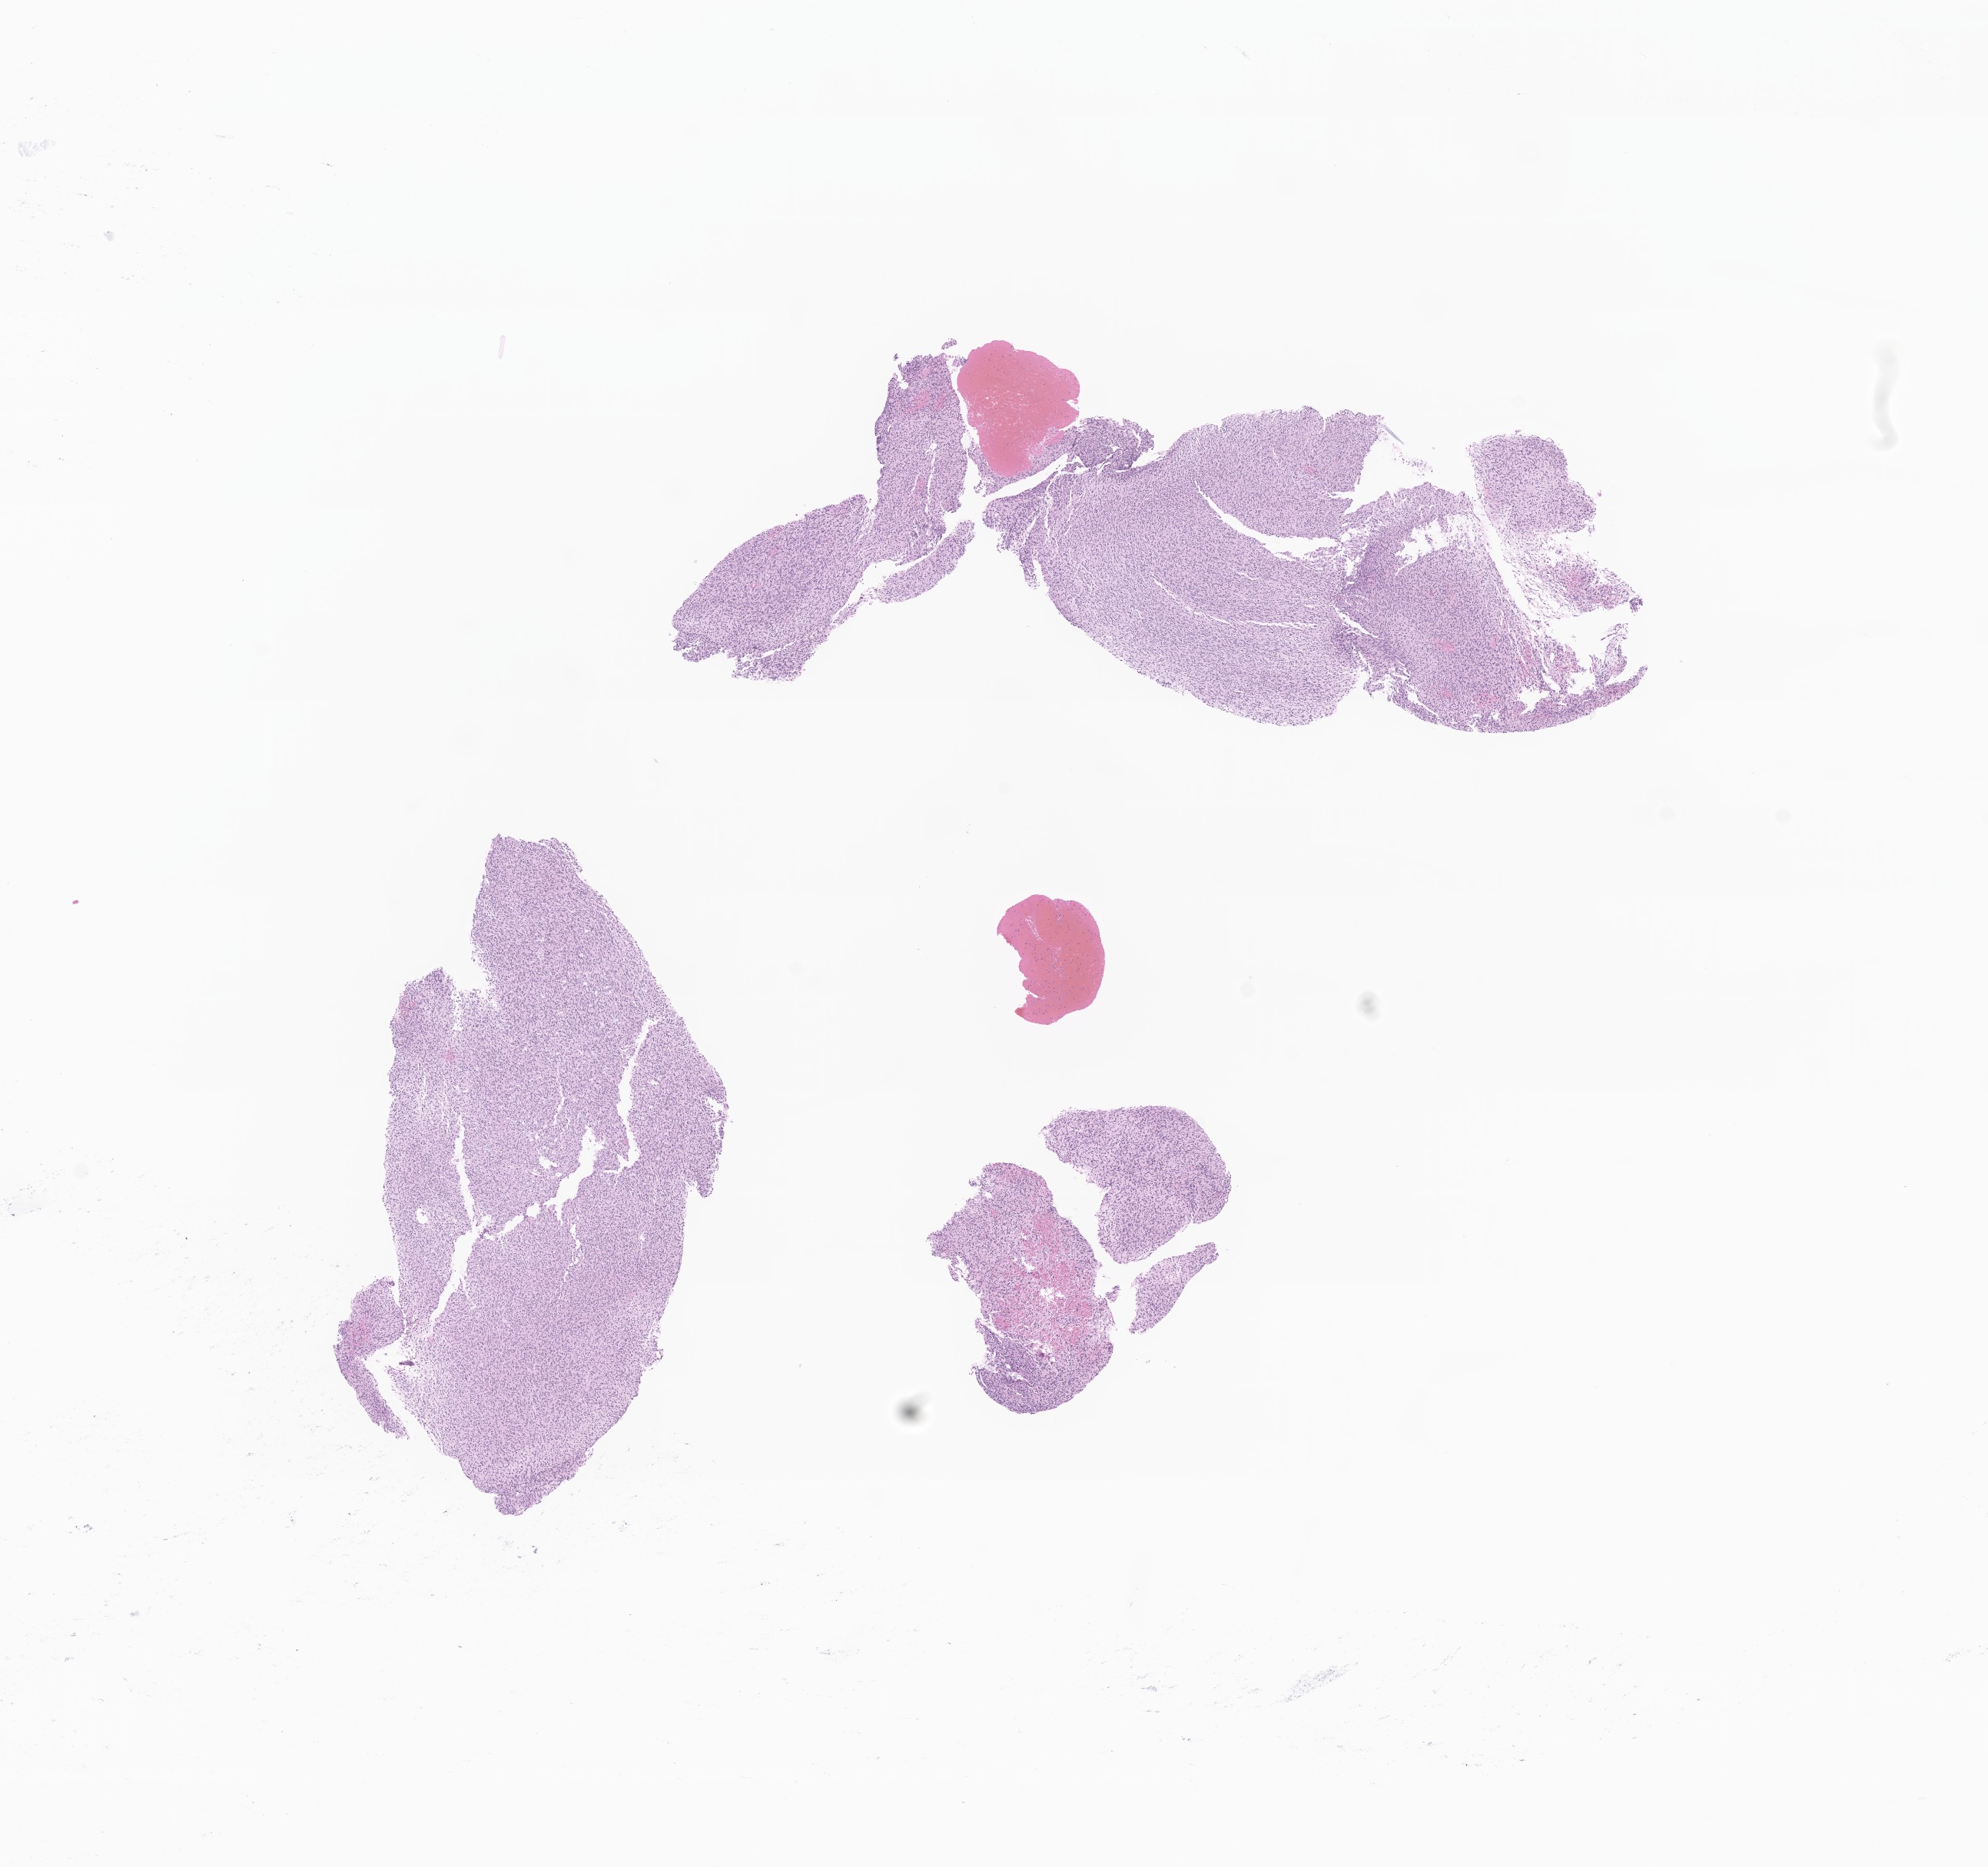
Whole-slide image, haematoxylin and eosin stain of tumor tissue from the brain, low-resolution overview of the scanned area, about 10.9 x 10.2 mm. Formalin-fixed, paraffin-embedded (FFPE) tissue. Patient female; age 58 months.
Diagnosis: Astrocytoma, NOS.